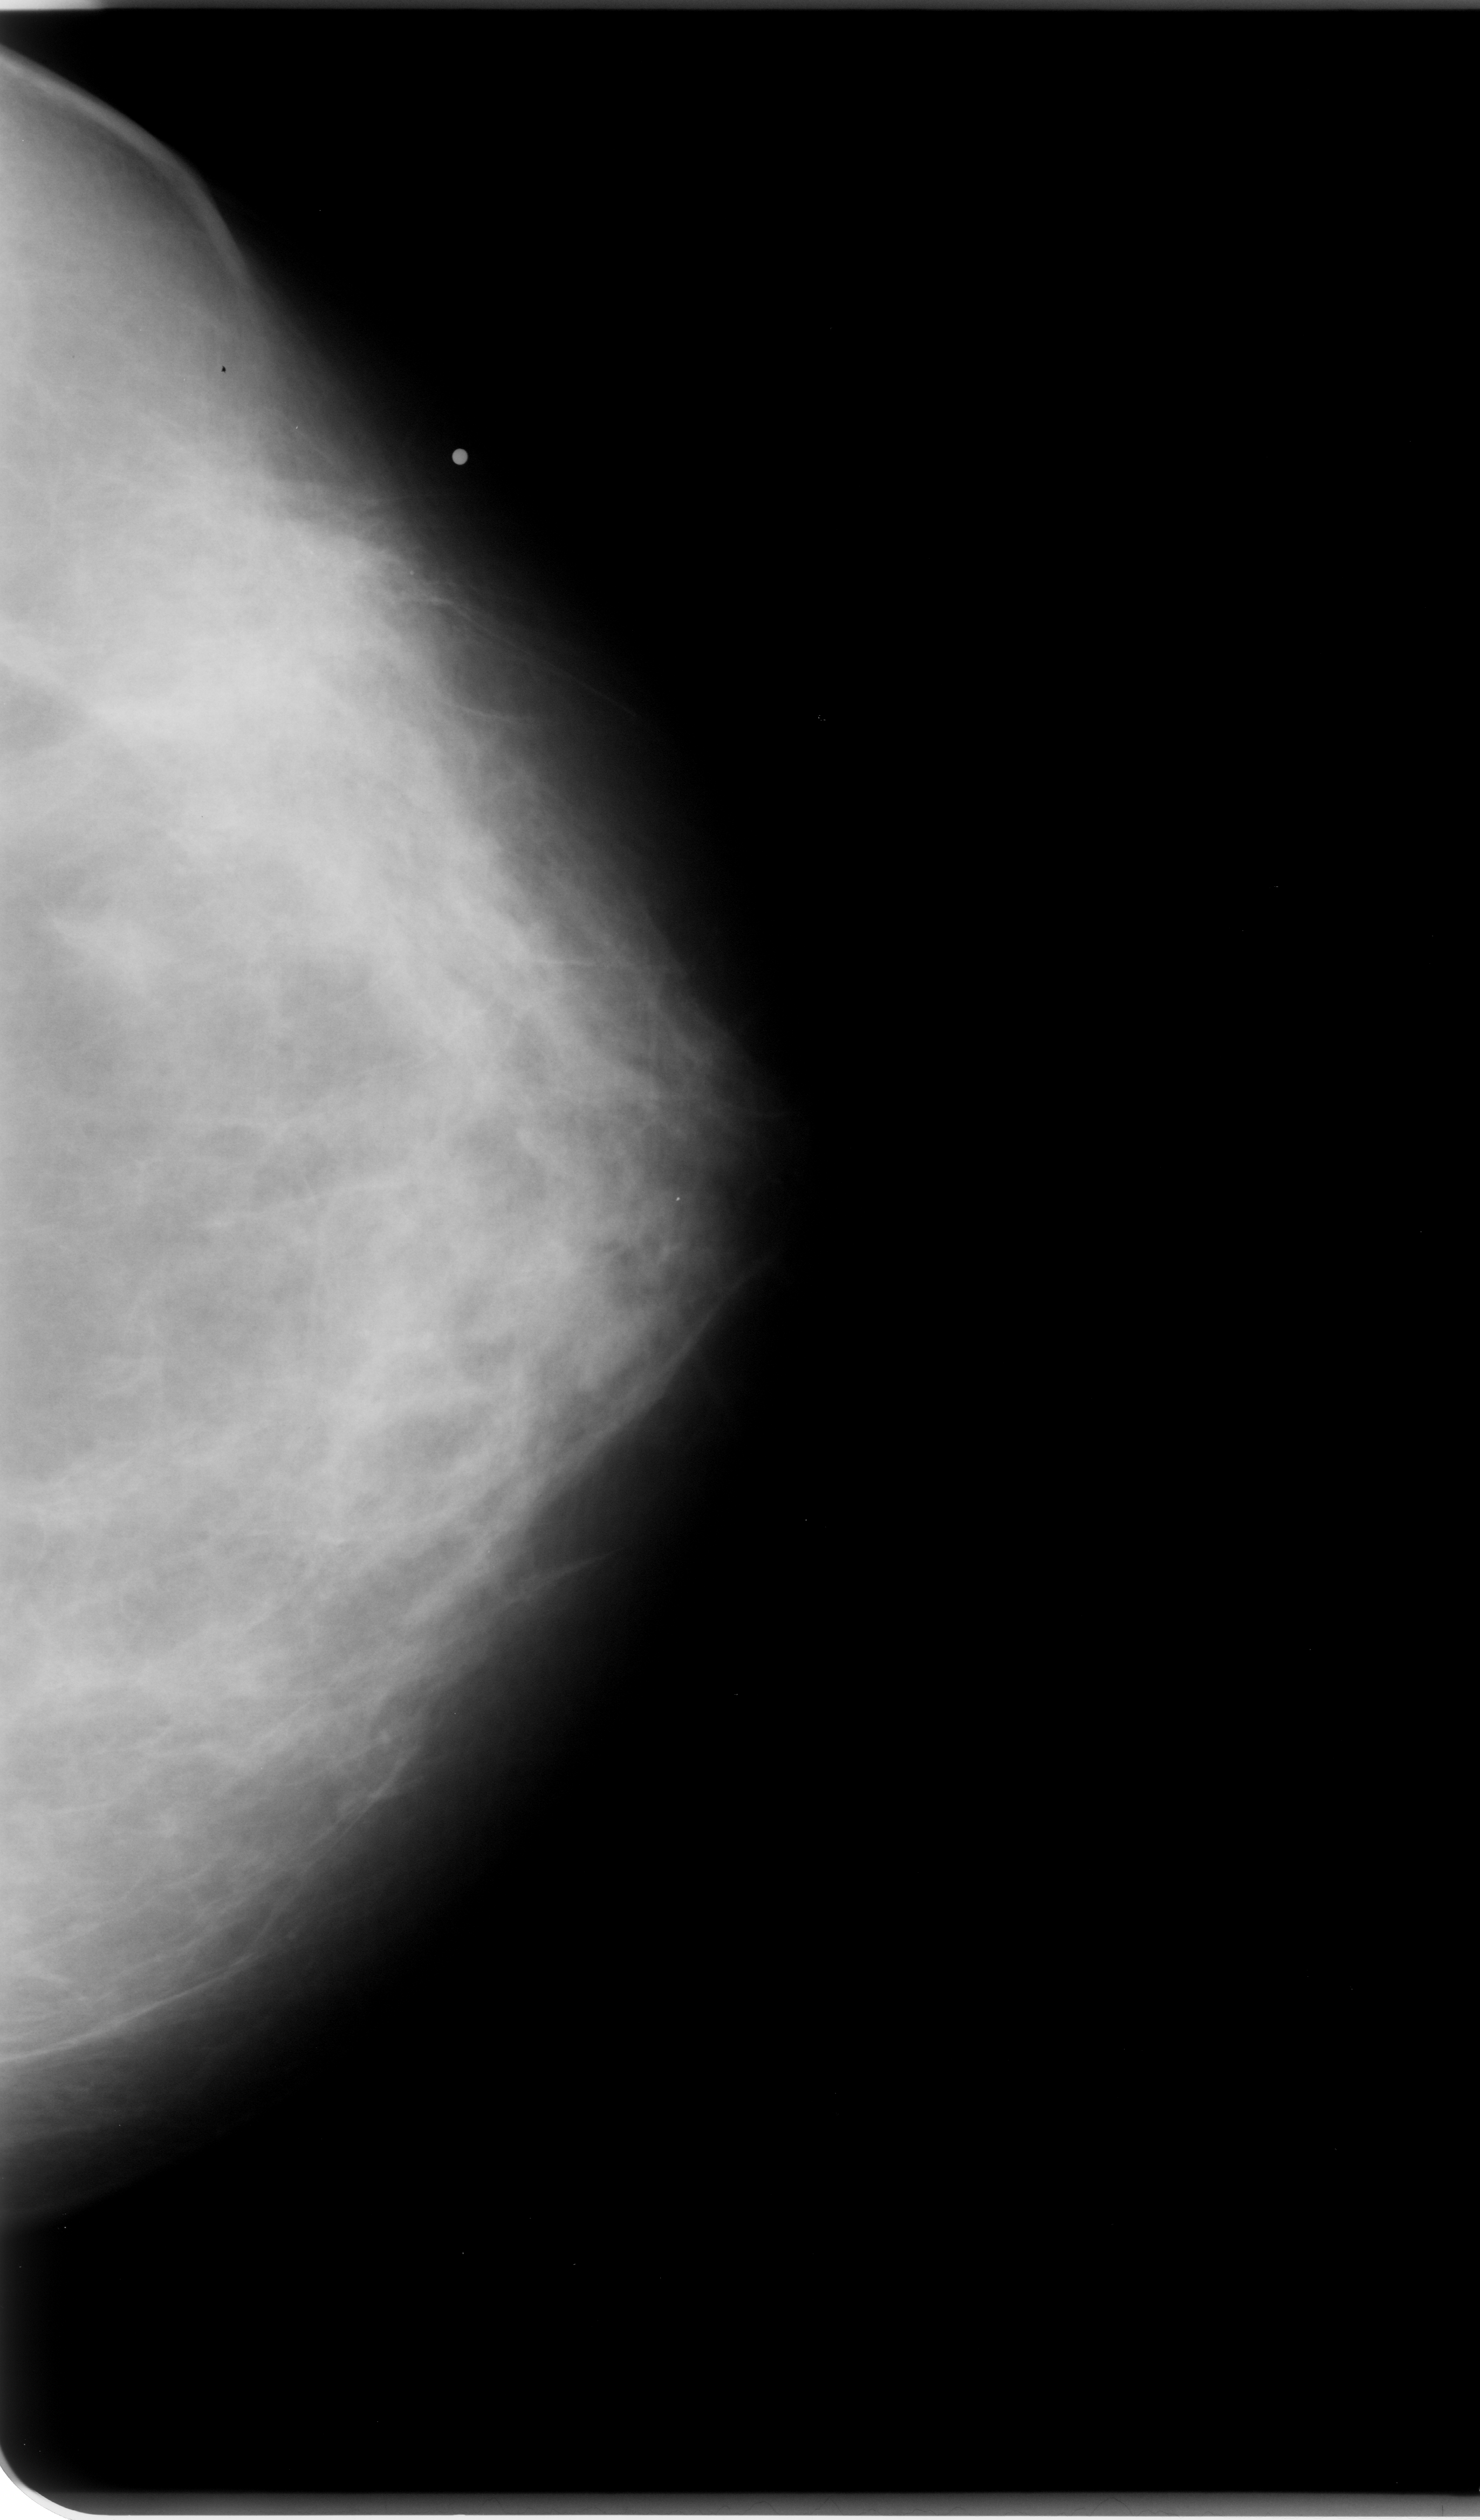
Digitized screen-film mammogram, left breast, CC view, BI-RADS breast density category 2 (scale 1–4).
Finding: calcifications, morphology amorphous, distribution clustered; BI-RADS assessment category 4; subtlety rating 2 on a 1 (subtle) to 5 (obvious) scale; pathology result (as recorded, not read from the image): malignant.